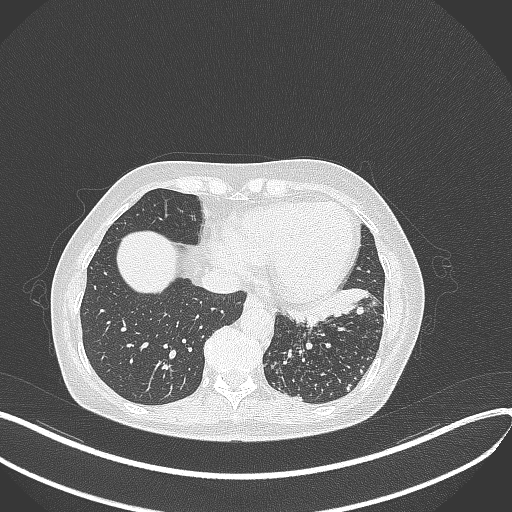
Chest CT, one axial slice. Slice 118 of 429 in the series (ordered by position). Lung window (W 1500 / L -600 HU). 1 mm slice thickness. 512 × 512 image matrix. Patient: female, 63 years. Case-level facts recorded for this patient, not image findings: clinical TNM (as recorded): T1b N0 M0; histopathological grade: G2-3.
Outlined on this slice (bounding box drawn by a radiologist):
- lung tumour (recorded histology: adenocarcinoma): bounding box [x1, y1, x2, y2] px = [283, 285, 370, 329]